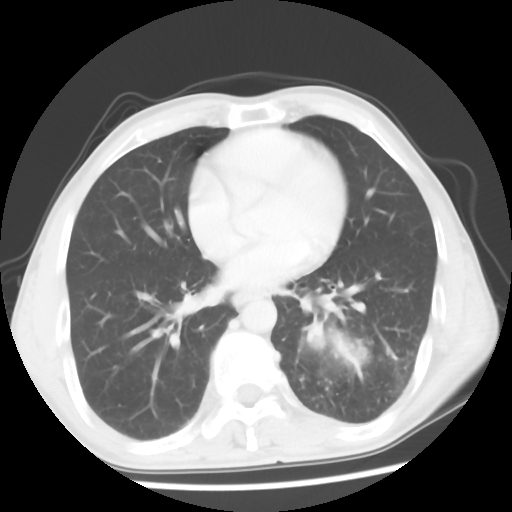
Chest CT, one axial slice; position 24 of 56 along the scan axis; reconstruction kernel STANDARD; lung window (W 1500 / L -600 HU); 5 mm slice thickness; 512 × 512 image matrix, field of view 318 × 318 mm. Male patient, age 60 years. From the clinical record (not read from this slice): clinical TNM (as recorded): T4 N0 M0.
Annotated regions visible in this slice (bounding box drawn by a radiologist):
- lung tumour (recorded histology: squamous cell carcinoma): box from (x=292, y=300) to (x=390, y=389) px